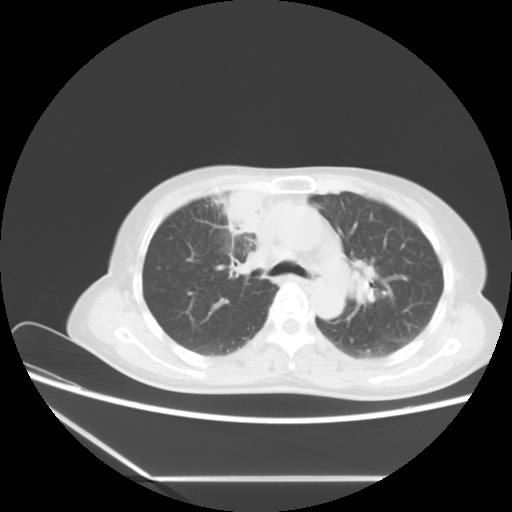
Chest CT, one axial slice. 120 kVp. Lung window (W 1500 / L -600 HU). 5 mm slice thickness. 512 × 512 image matrix, field of view 350 × 350 mm. Patient: female, 63 years. From the clinical record (not read from this slice): clinical TNM (as recorded): T2b N1 M0.
Structures marked on this image (bounding box drawn by a radiologist):
- lung tumour (recorded histology: adenocarcinoma): bounding box <226,178,264,242> (left, top, right, bottom; pixels)